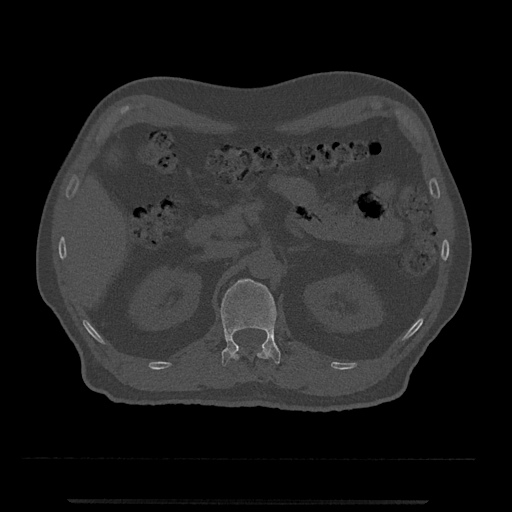
CT including the spine, one axial slice. Reconstruction kernel Br40s/3. 120 kVp. Bone window (W 1800 / L 400 HU). 512 × 512 image matrix. Male patient, age 63 years. From the clinical record (not read from this slice): primary cancer: prostate.
Outlined on this slice (semi-automatically segmented with operator editing):
- L1 vertebra: bounding box (x1, y1, x2, y2) in pixels: (220, 278, 281, 366)
- T12 vertebra: (231, 346, 270, 360)